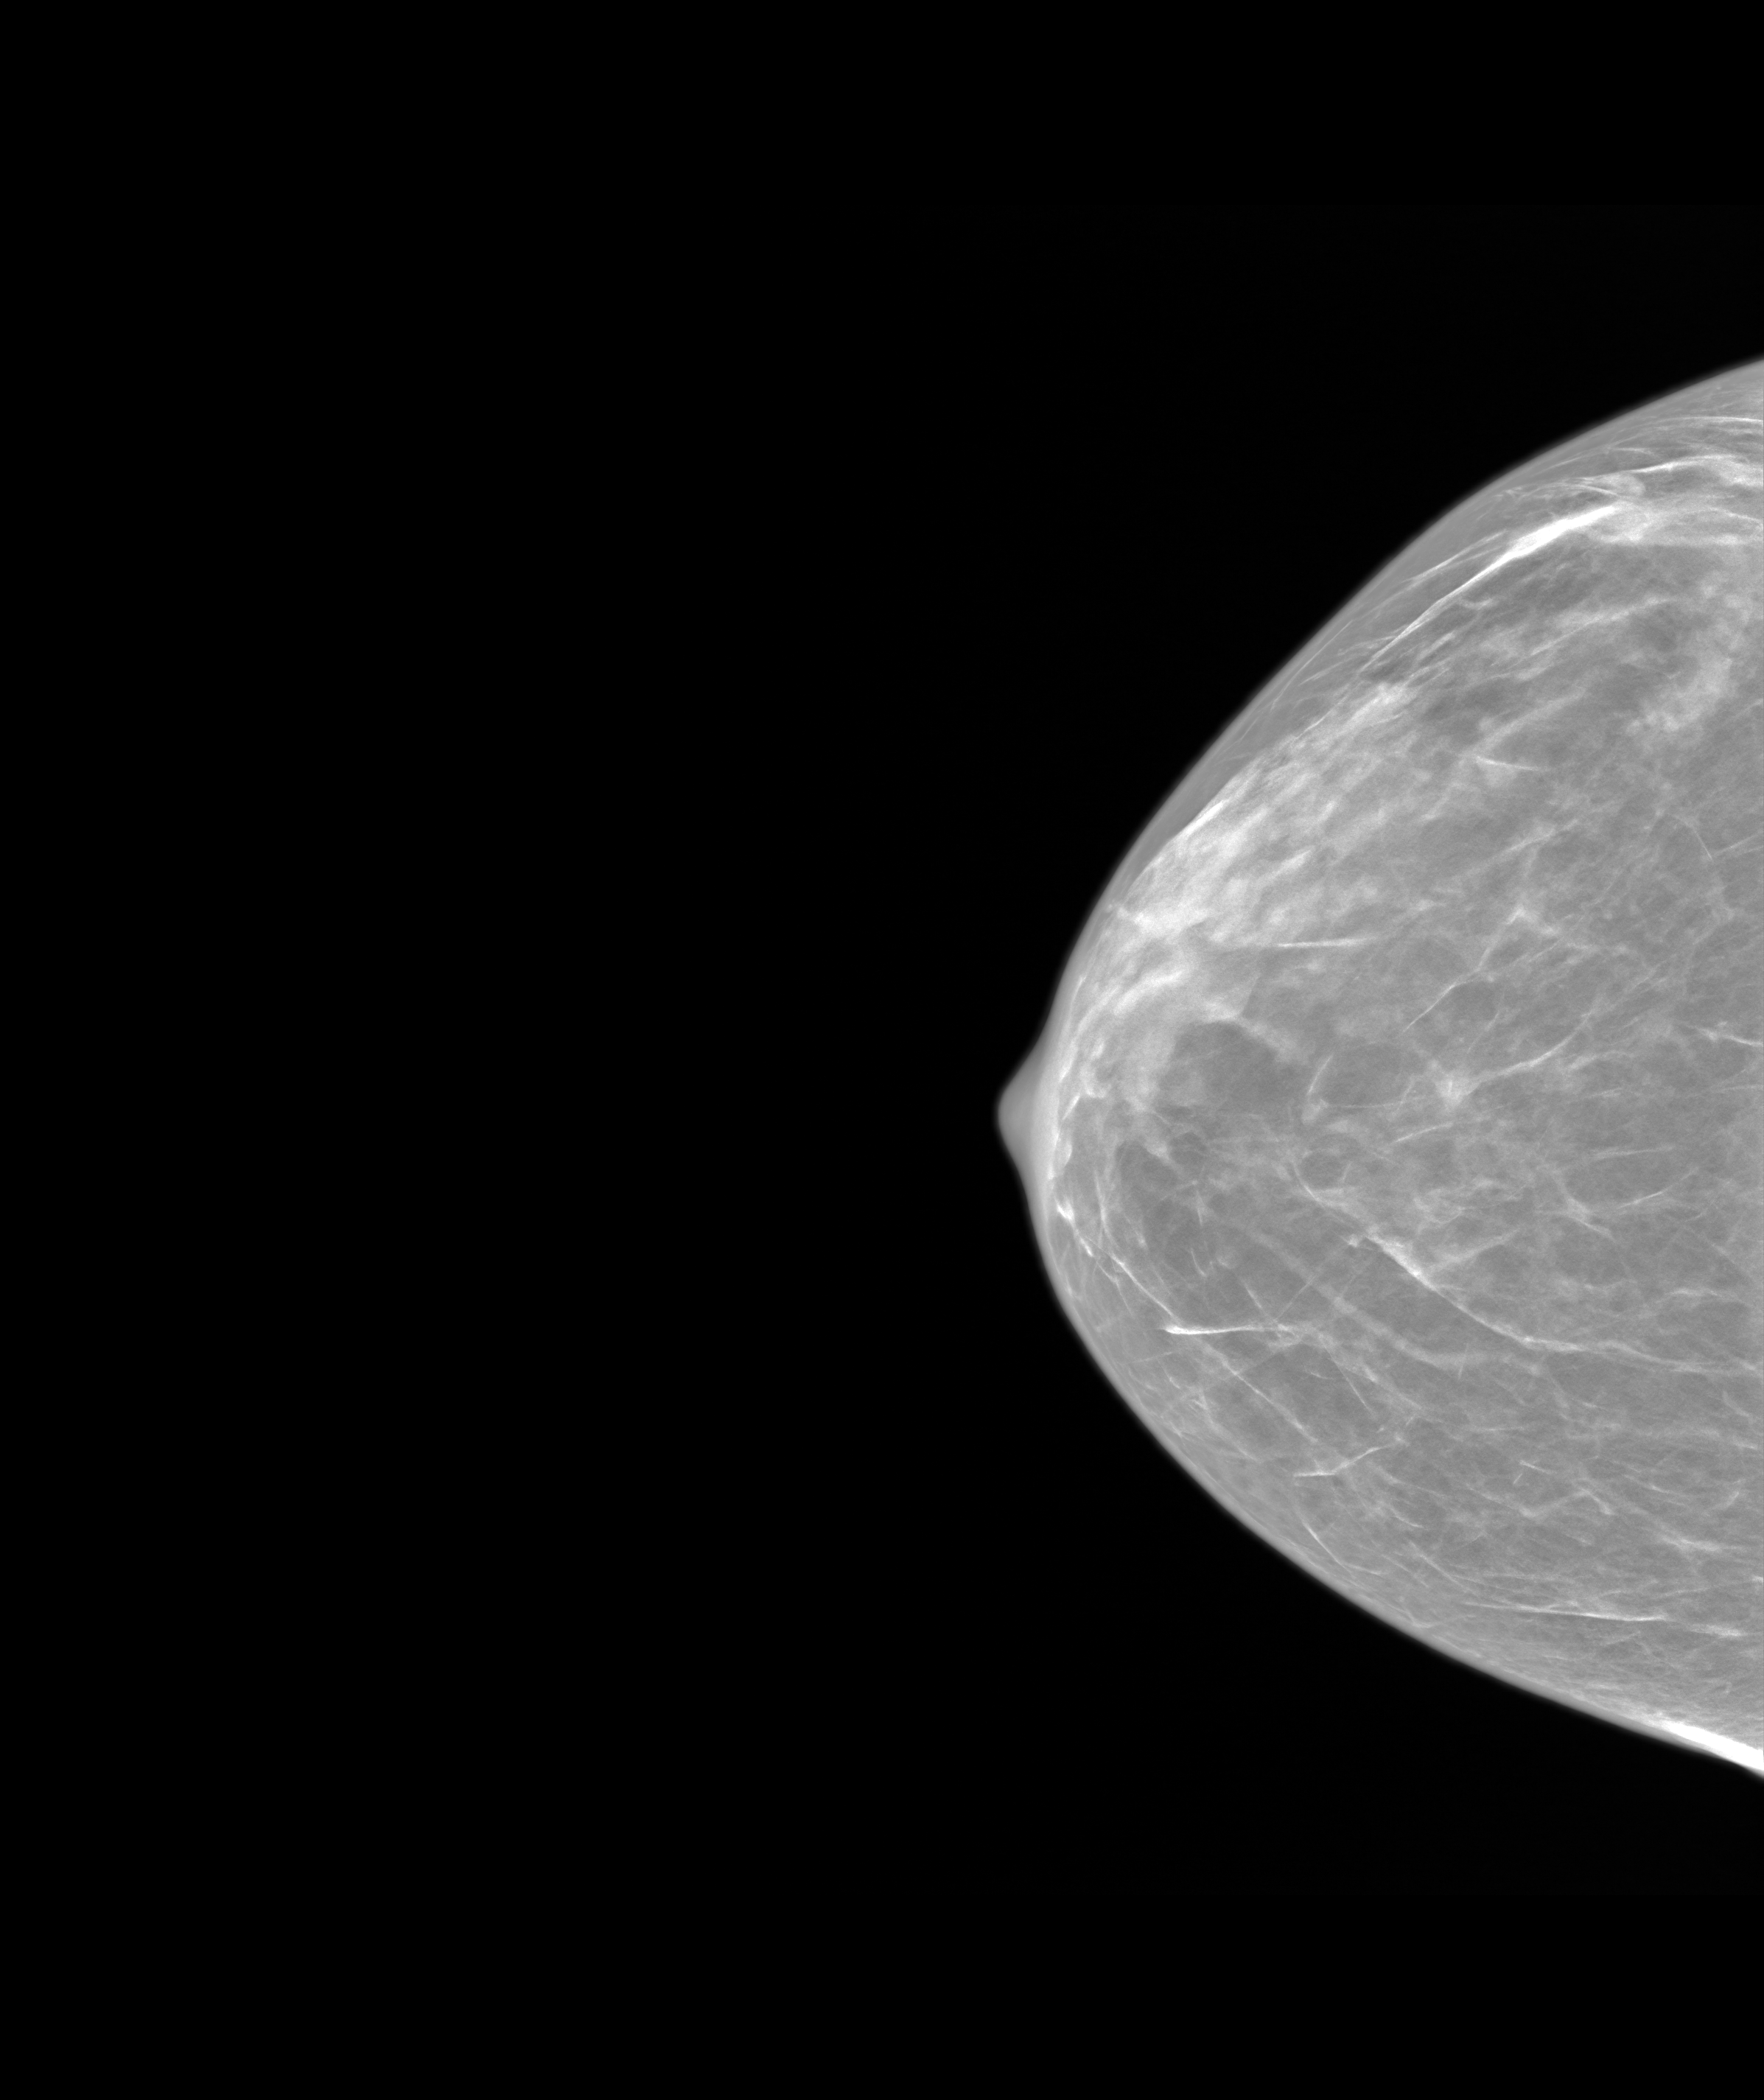
Synthetic 2-D view generated from a tomosynthesis acquisition (not an FFDM exposure), right breast, CC view, screening examination, system: SenoIris_1SP1.2(425). Female patient, age 43 years.
Breast density at the screening exam (both breasts): heterogeneously dense (BI-RADS density category c). Final BI-RADS assessment for this screening round (tomosynthesis exam, both breasts): category 1. Recall: no recall after this screen.